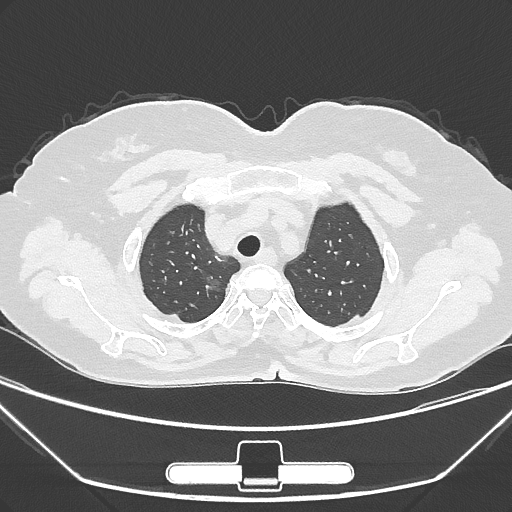
Chest CT, one axial slice; slice 235 of 275 in the series (ordered by position); reconstruction kernel IMR1,SharpPlus; 120 kVp; lung window (W 1500 / L -600 HU); 1 mm slice thickness; 512 × 512 image matrix, field of view 356 × 356 mm. Female patient, age 63 years. Case-level facts recorded for this patient, not image findings: clinical TNM (as recorded): T1a N0 M0.
Outlined on this slice (bounding box drawn by a radiologist):
- lung tumour (recorded histology: adenocarcinoma): bounding box (x1, y1, x2, y2) in pixels: (196, 271, 226, 295)